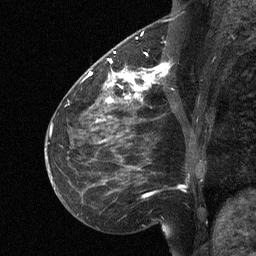
Breast MRI (dynamic contrast-enhanced), one sagittal slice. Position 24 of 64 along the scan axis. Dynamic contrast-enhanced study with each time point stored as its own series, time point 2 of 3 at this slice position (early post-contrast, ordered by acquisition time). 1.5 T. TE 4.8 ms, TR 27 ms. 256 × 256 image matrix, field of view 200 × 200 mm. Patient: female, 51 years. From the clinical record (not read from this slice): setting: breast cancer imaged before/during neoadjuvant chemotherapy; receptor status: HR-positive, HER2-negative.
Annotated regions visible in this slice (semi-automatic segmentation, software-assisted and operator-edited):
- analysis volume of interest (the breast-tissue region the enhancement analysis was run in; not a lesion): bounding box (x1, y1, x2, y2) in pixels: (112, 46, 169, 106)
- tumour enhancement mask (voxels above the 90 % enhancement threshold inside the analysis volume of interest): (112, 52, 169, 102)